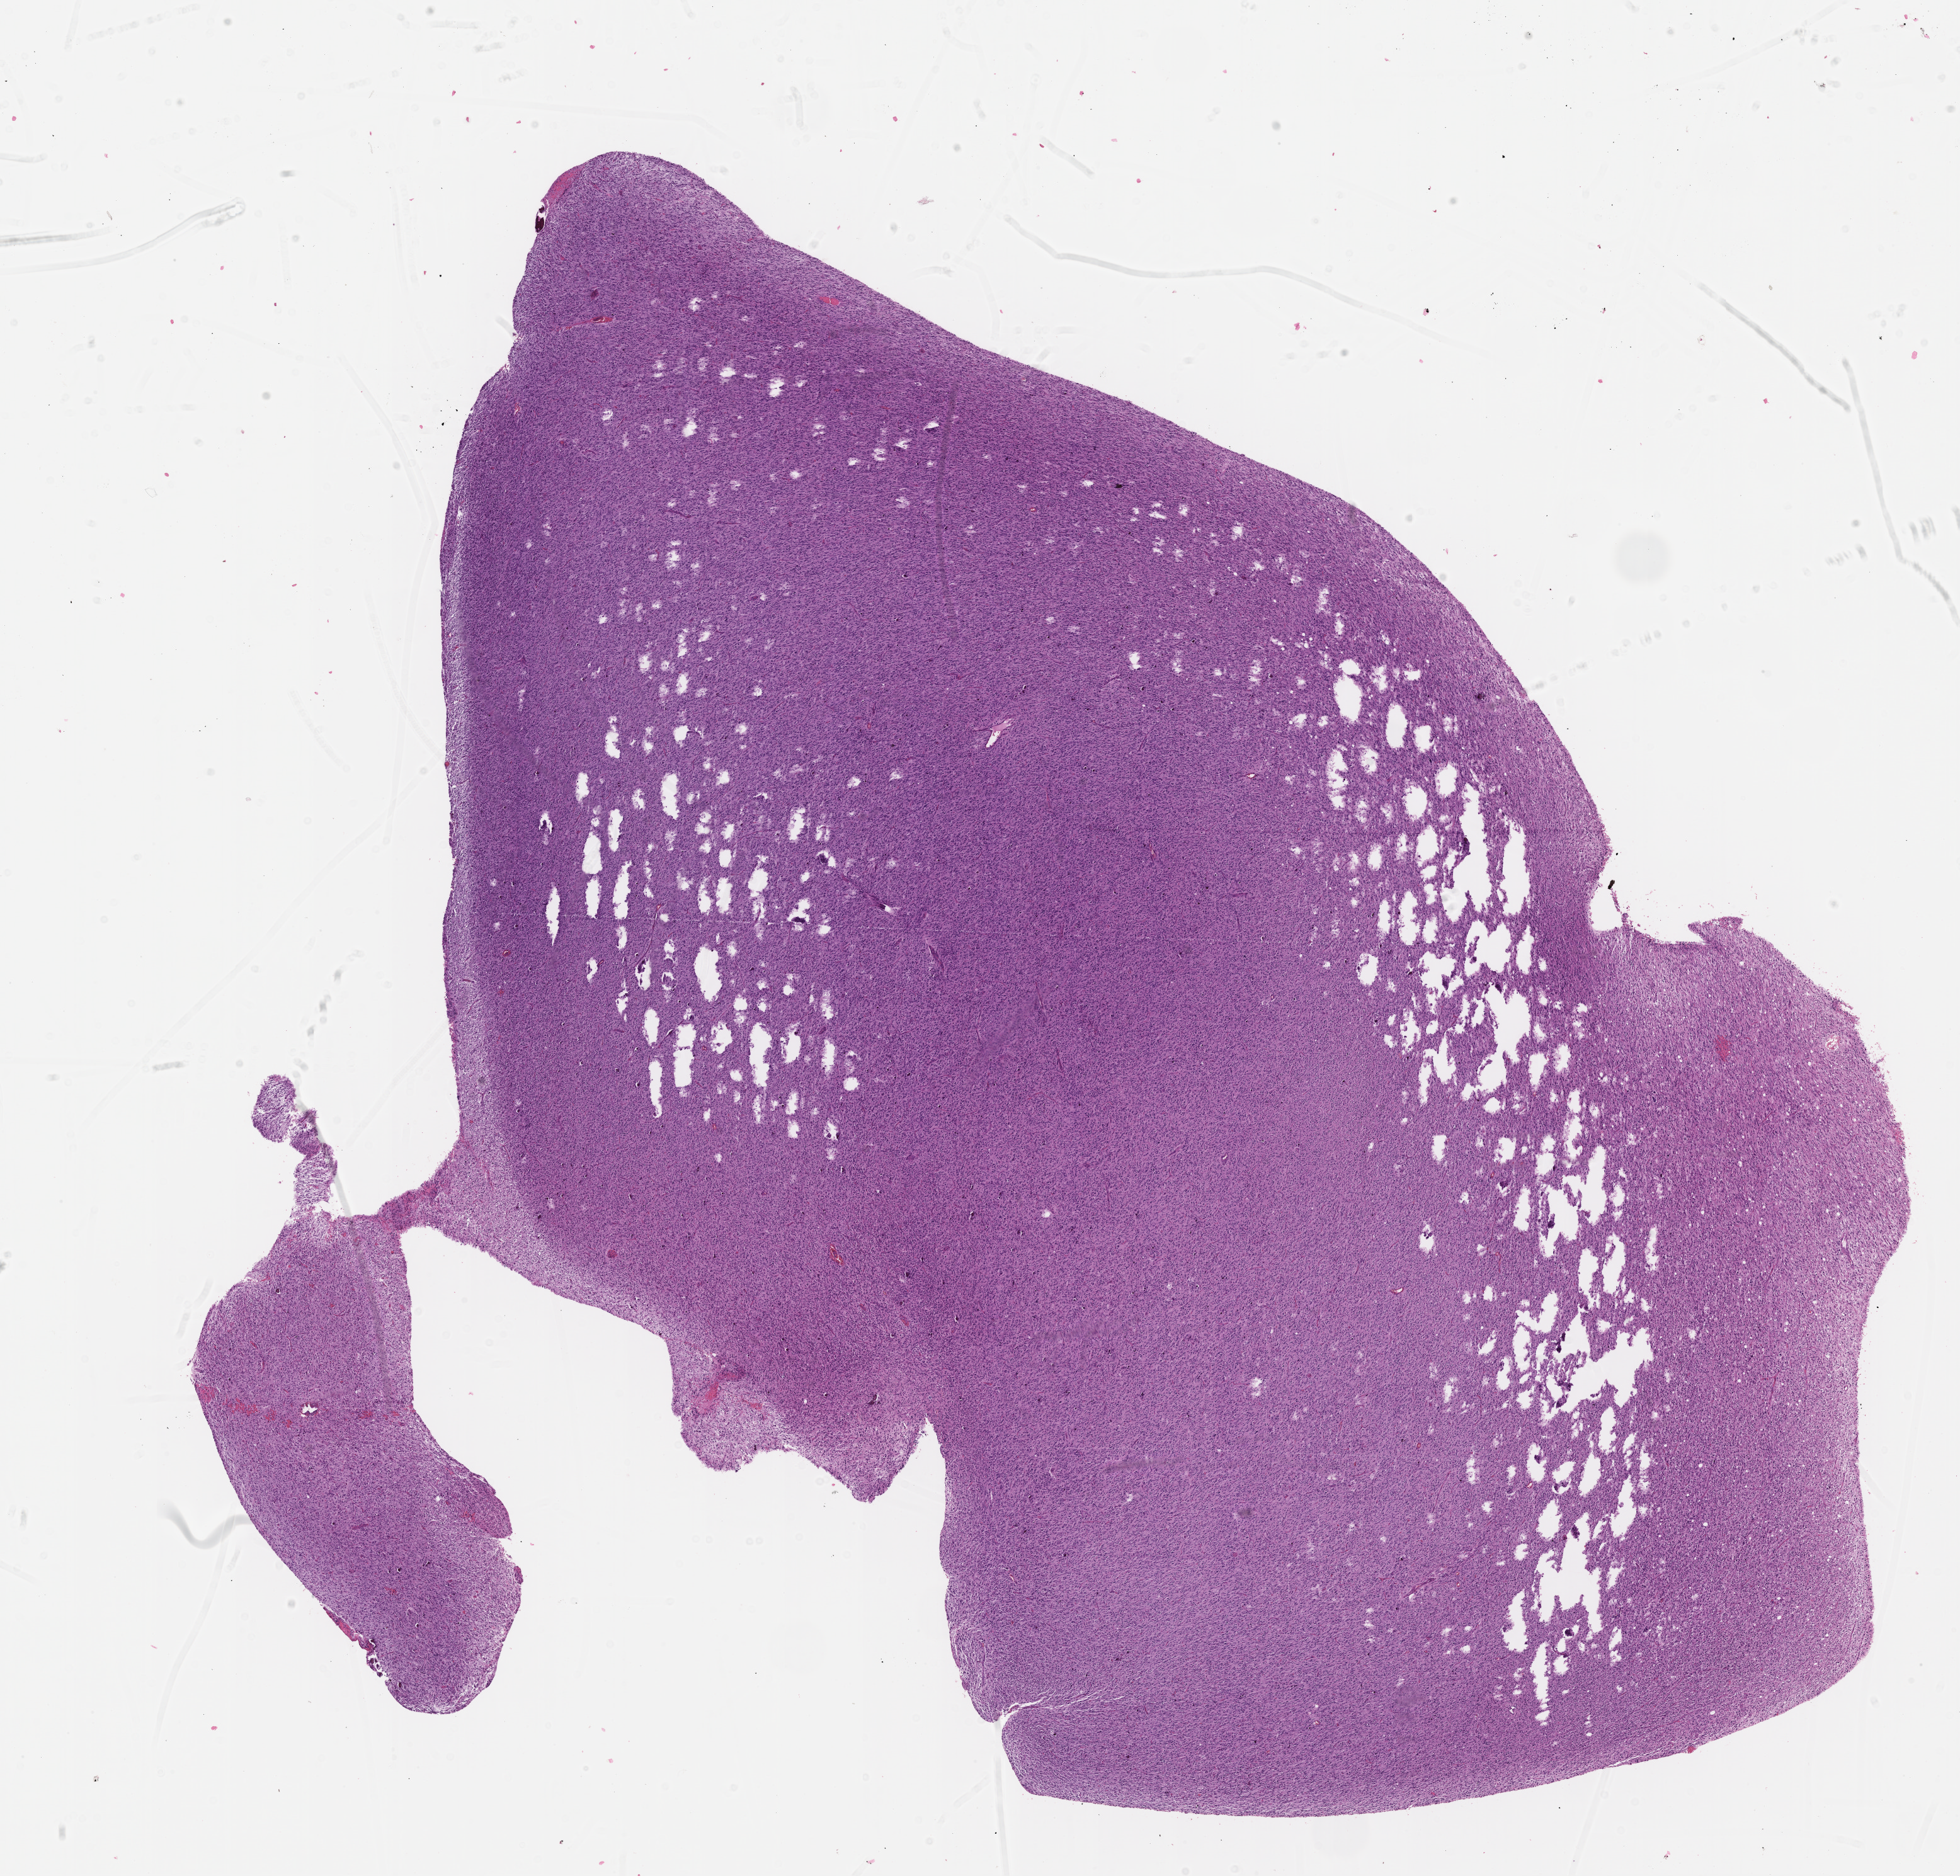
Whole-slide histology image, H&E-stained — whole scanned area (about 12.6 x 12.1 mm) shown as a low-resolution overview, FFPE section, sample: primary tumour, brain. Male patient; age at initial diagnosis 50 years.
• diagnosis: Glioblastoma